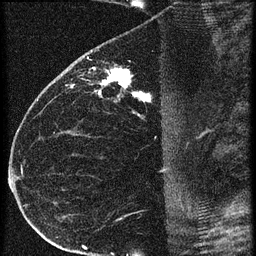
Breast MRI (dynamic contrast-enhanced), one sagittal slice. Position 34 of 60 along the scan axis. 3 images stored at this slice position (order not interpretable as contrast timing). 1.5 T. TE 4.2 ms, TR 20.4 ms. 1.5 mm slice thickness. 256 × 256 image matrix. Female patient, age 35 years. From the clinical record (not read from this slice): setting: breast cancer imaged before/during neoadjuvant chemotherapy; receptor status: HR-positive, HER2-negative.
Annotated regions visible in this slice (semi-automatic segmentation, software-assisted and operator-edited):
- analysis volume of interest (the breast-tissue region the enhancement analysis was run in; not a lesion): bounding box [x1, y1, x2, y2] px = [65, 60, 169, 119]
- tumour enhancement mask (voxels above the 90 % enhancement threshold inside the analysis volume of interest): [71, 68, 150, 101]